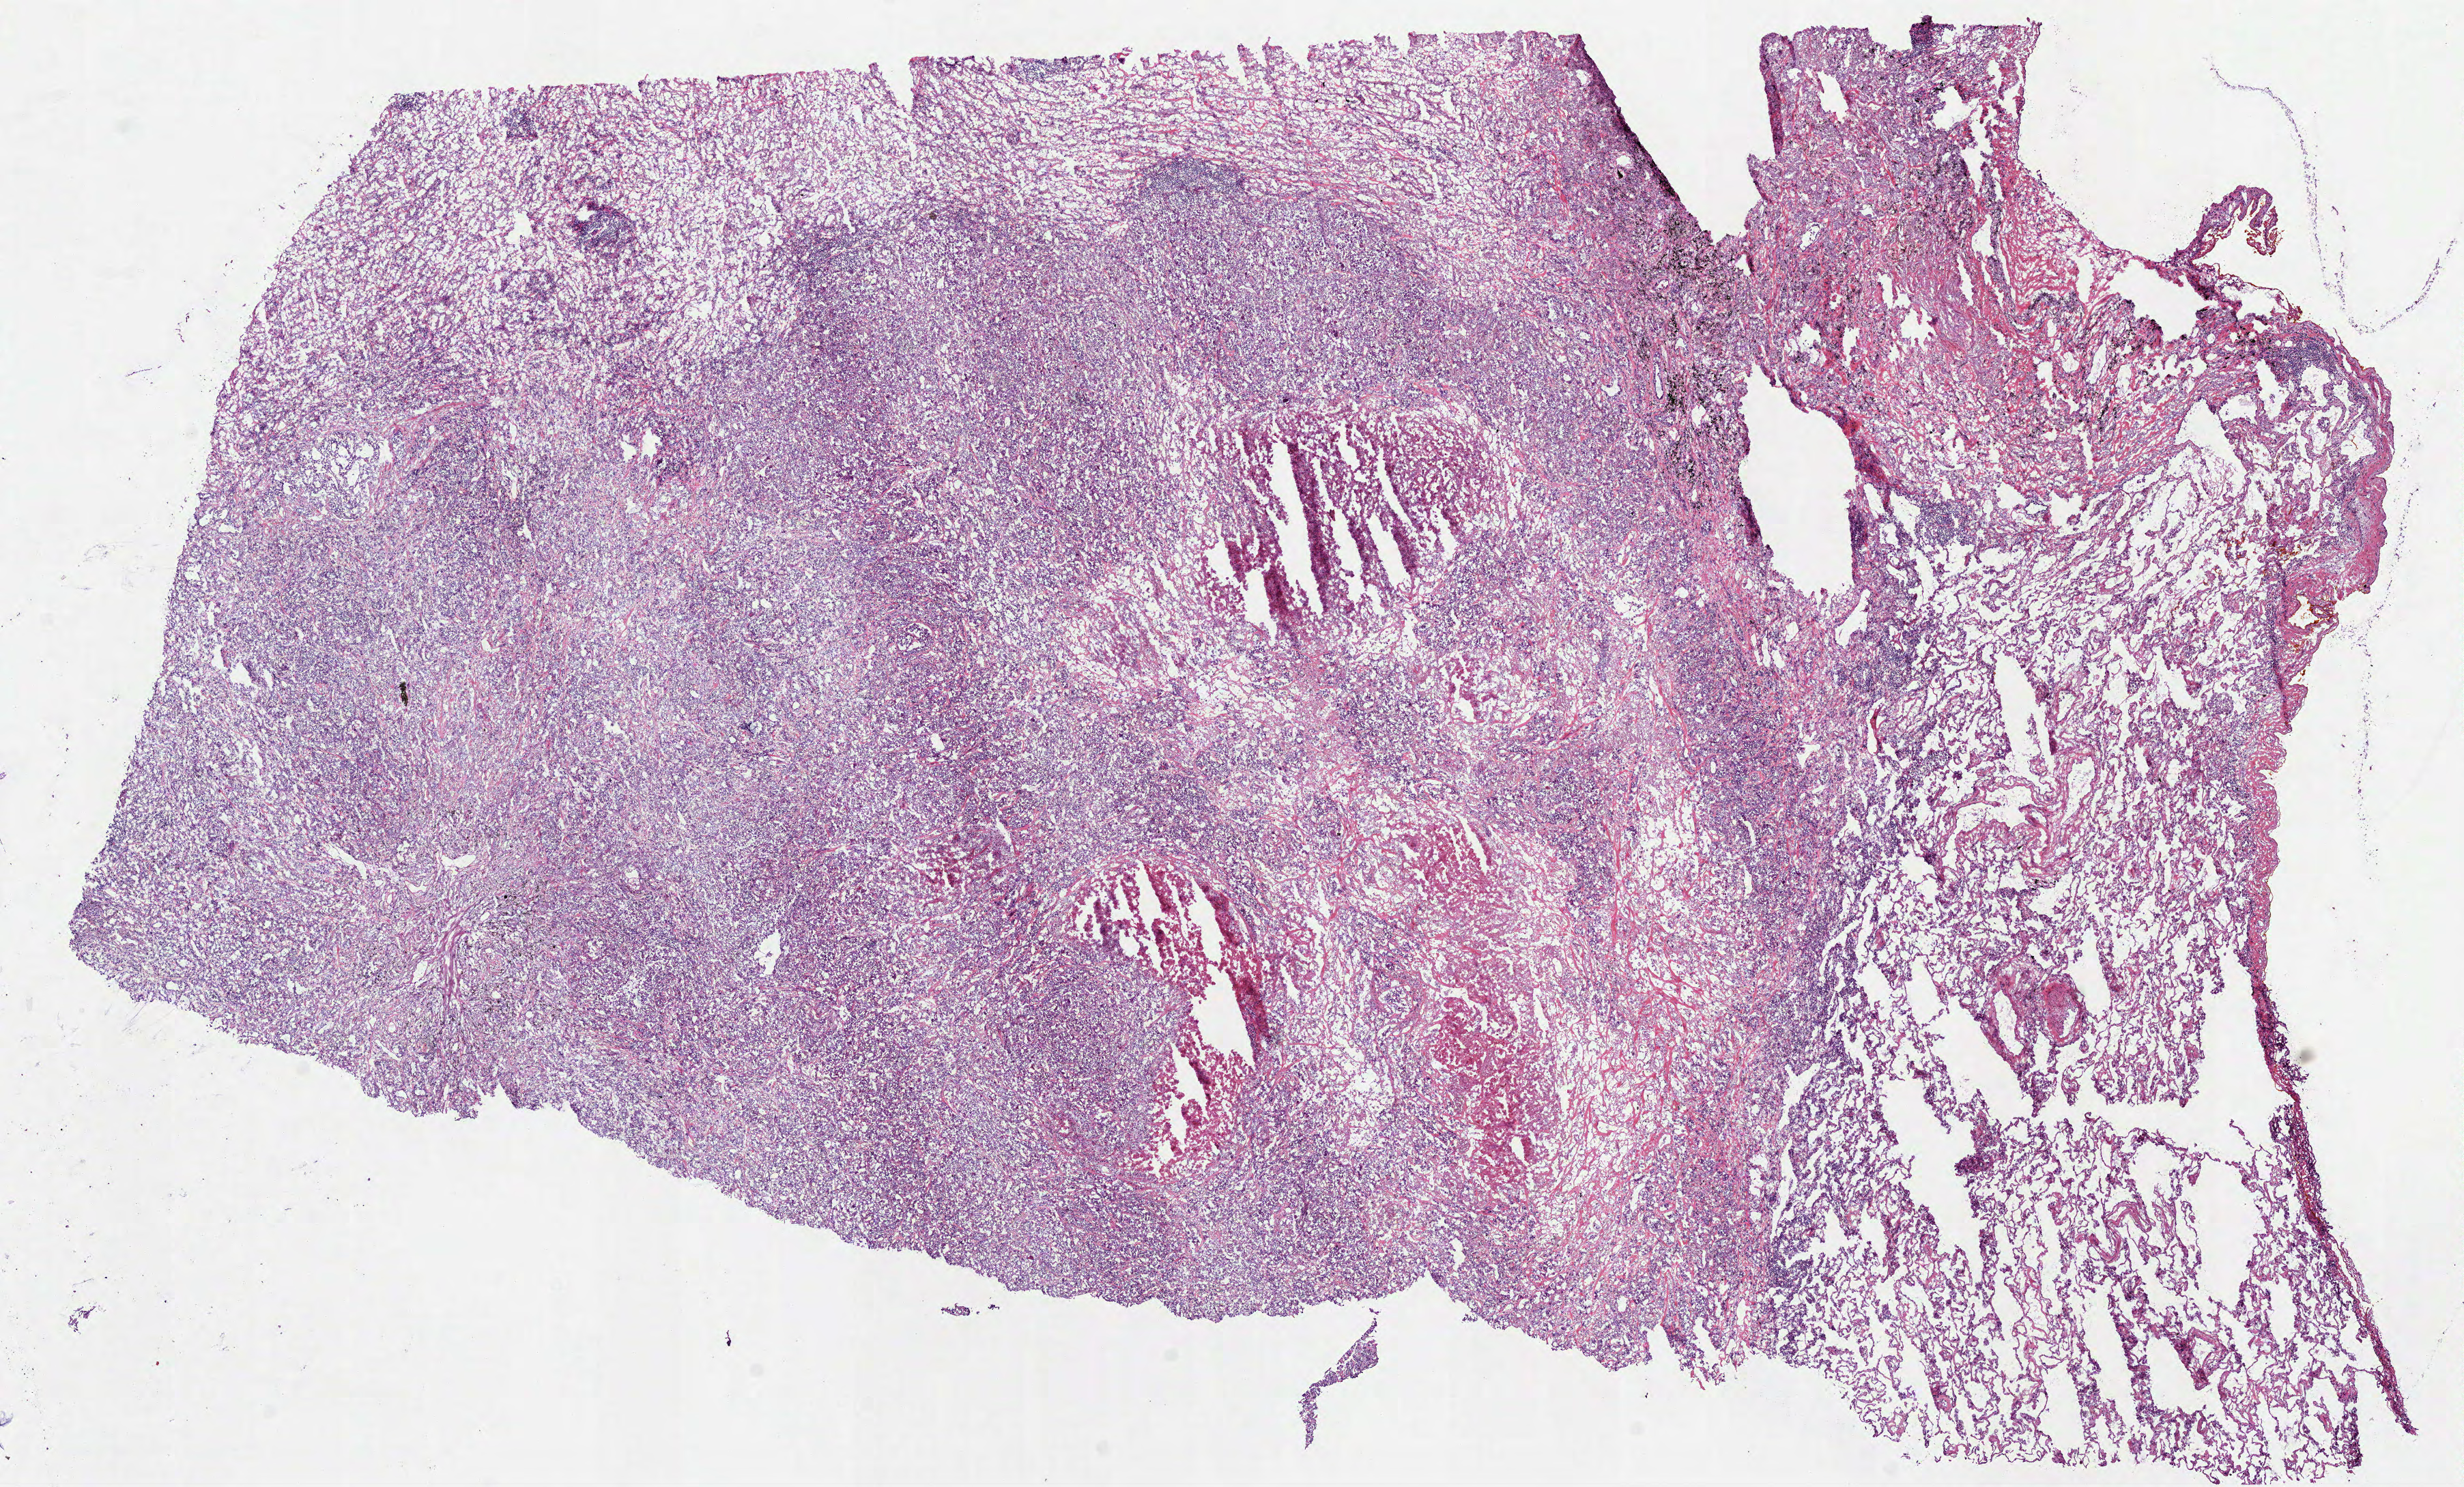
Whole-slide histology image, H&E-stained — low-resolution overview of the scanned area, about 14.6 x 8.8 mm (slide scanned at 40x). Frozen section from the top of the tissue portion. Sample: primary tumour, lung. Male, age 85 years at initial diagnosis. Composition of this section per pathologist review: tumour cells 71%, tumour nuclei 71%, normal cells 16%, stromal cells 3%, necrosis 10%. Inflammatory infiltration, as recorded: lymphocyte infiltration 10%, monocyte infiltration 10%, neutrophil infiltration 2%.
* diagnosis: Adenocarcinoma with mixed subtypes
* laterality: right
* AJCC pathologic stage: IB